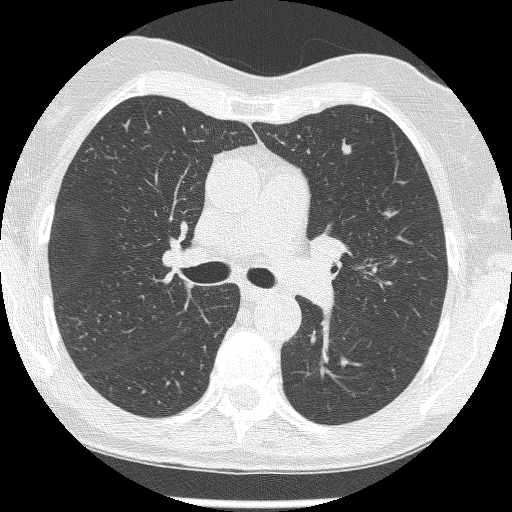
Low-dose screening chest CT, axial slice. Second screening round (one year after baseline). Lung window (W 1500 / L -600 HU). 1.25 mm slice thickness. Female, age 60 years at enrolment. Current smoker at enrolment.
Expert-annotated lung lesion, bounding box [x1, y1, x2, y2] px = [335, 139, 361, 163]. The screening reader recorded 2 non-calcified nodules or masses ≥4 mm on this exam (left upper lobe, left upper lobe); which of them this box marks is not recorded. Official screen result: positive, change unspecified: nodule(s) >= 4 mm or enlarging nodule(s), mass(es), or other non-specific abnormalities suspicious for lung cancer. Later outcome: lung cancer diagnosed 428 days after this screen — adenocarcinoma, NOS, left upper lobe, moderately differentiated (G2), stage IA (AJCC 6th edition), 6 mm at pathology.